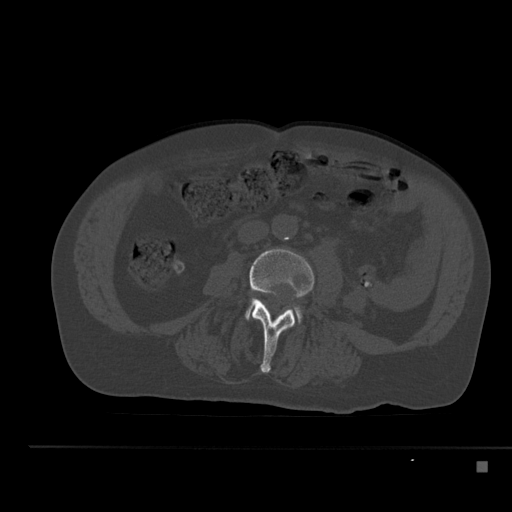
CT including the spine, one axial slice. Slice 159 of 517 in the series (ordered by position). 120 kVp. Bone window (W 1800 / L 400 HU). 1.5 mm slice thickness. 512 × 512 image matrix, field of view 408 × 408 mm. Patient: male, 70 years. Case-level facts recorded for this patient, not image findings: primary cancer: renal.
Outlined on this slice (semi-automatically segmented with operator editing):
- L3 vertebra: bounding box (x1, y1, x2, y2) in pixels: (249, 249, 314, 373)
- L4 vertebra: (246, 304, 301, 320)